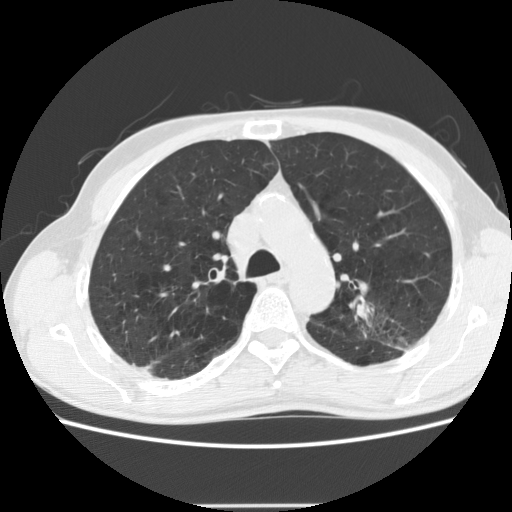
Low-dose screening chest CT, one axial slice. Position 138 of 191 along the scan axis. Reconstruction kernel STANDARD. Lung window (W 1500 / L -600 HU). 512 × 512 image matrix.
Outlined on this slice (outlined manually by an expert reader):
- lesion 1 (tumor, upper lobe of left lung): box from (x=356, y=303) to (x=372, y=320) px